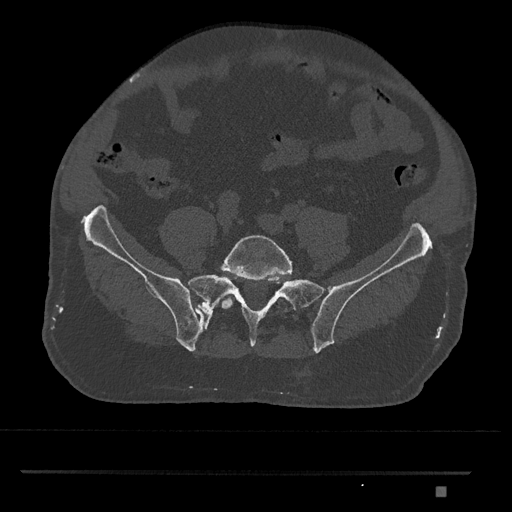
CT including the spine, one axial slice; position 526 of 1134 along the scan axis; bone window (W 1800 / L 400 HU); 0.5 mm slice thickness; 512 × 512 image matrix, field of view 429 × 429 mm. Male patient, age 65 years. From the clinical record (not read from this slice): primary cancer: prostate.
Annotated regions visible in this slice (semi-automatically segmented with operator editing):
- L5 vertebra: box from (x=221, y=235) to (x=292, y=311) px